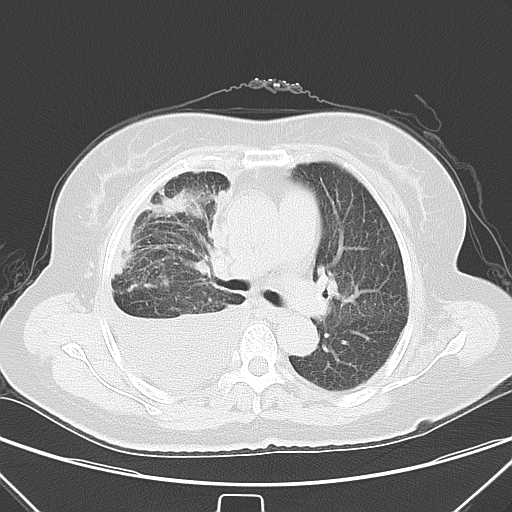
Chest CT, one axial slice. Position 37 of 55 along the scan axis. Lung window (W 1500 / L -600 HU). 5 mm slice thickness. 512 × 512 image matrix, field of view 352 × 352 mm. Female patient, age 66 years. Case-level facts recorded for this patient, not image findings: clinical TNM (as recorded): T2 N0 M1.
Structures marked on this image (bounding box drawn by a radiologist):
- lung tumour (recorded histology: adenocarcinoma): bounding box [x1, y1, x2, y2] px = [160, 185, 200, 221]